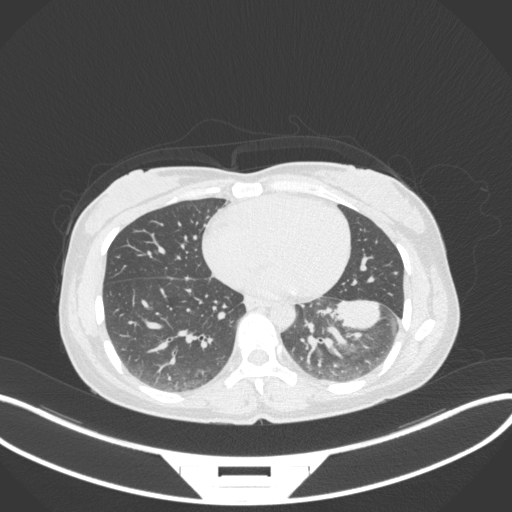
Chest CT, one axial slice. Slice 140 of 361 in the series (ordered by position). 120 kVp. Lung window (W 1500 / L -600 HU). 1 mm slice thickness. 512 × 512 image matrix, field of view 400 × 400 mm. Female patient, age 41 years. Case-level facts recorded for this patient, not image findings: clinical TNM (as recorded): T2a N3 M1b.
Structures marked on this image (bounding box drawn by a radiologist):
- lung tumour (recorded histology: adenocarcinoma): bounding box [x1, y1, x2, y2] px = [334, 298, 390, 335]